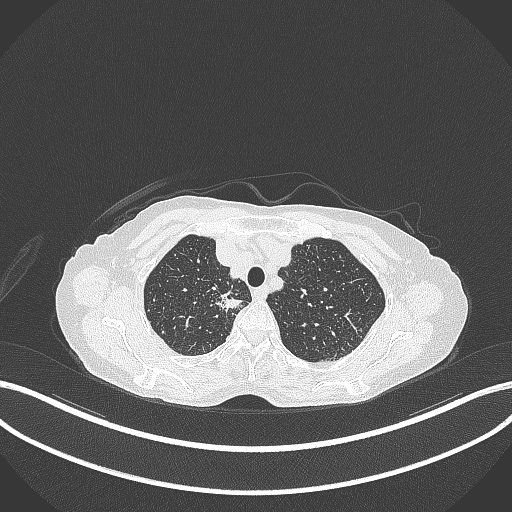
Chest CT, one axial slice. Slice 307 of 403 in the series (ordered by position). 120 kVp. Lung window (W 1500 / L -600 HU). 1 mm slice thickness. 512 × 512 image matrix, field of view 400 × 400 mm. Patient: female, 75 years. From the clinical record (not read from this slice): clinical TNM (as recorded): T1c N1 M1.
Structures marked on this image (rectangle marked by the reading radiologist):
- lung tumour (recorded histology: adenocarcinoma): bounding box (x1, y1, x2, y2) in pixels: (213, 291, 243, 312)